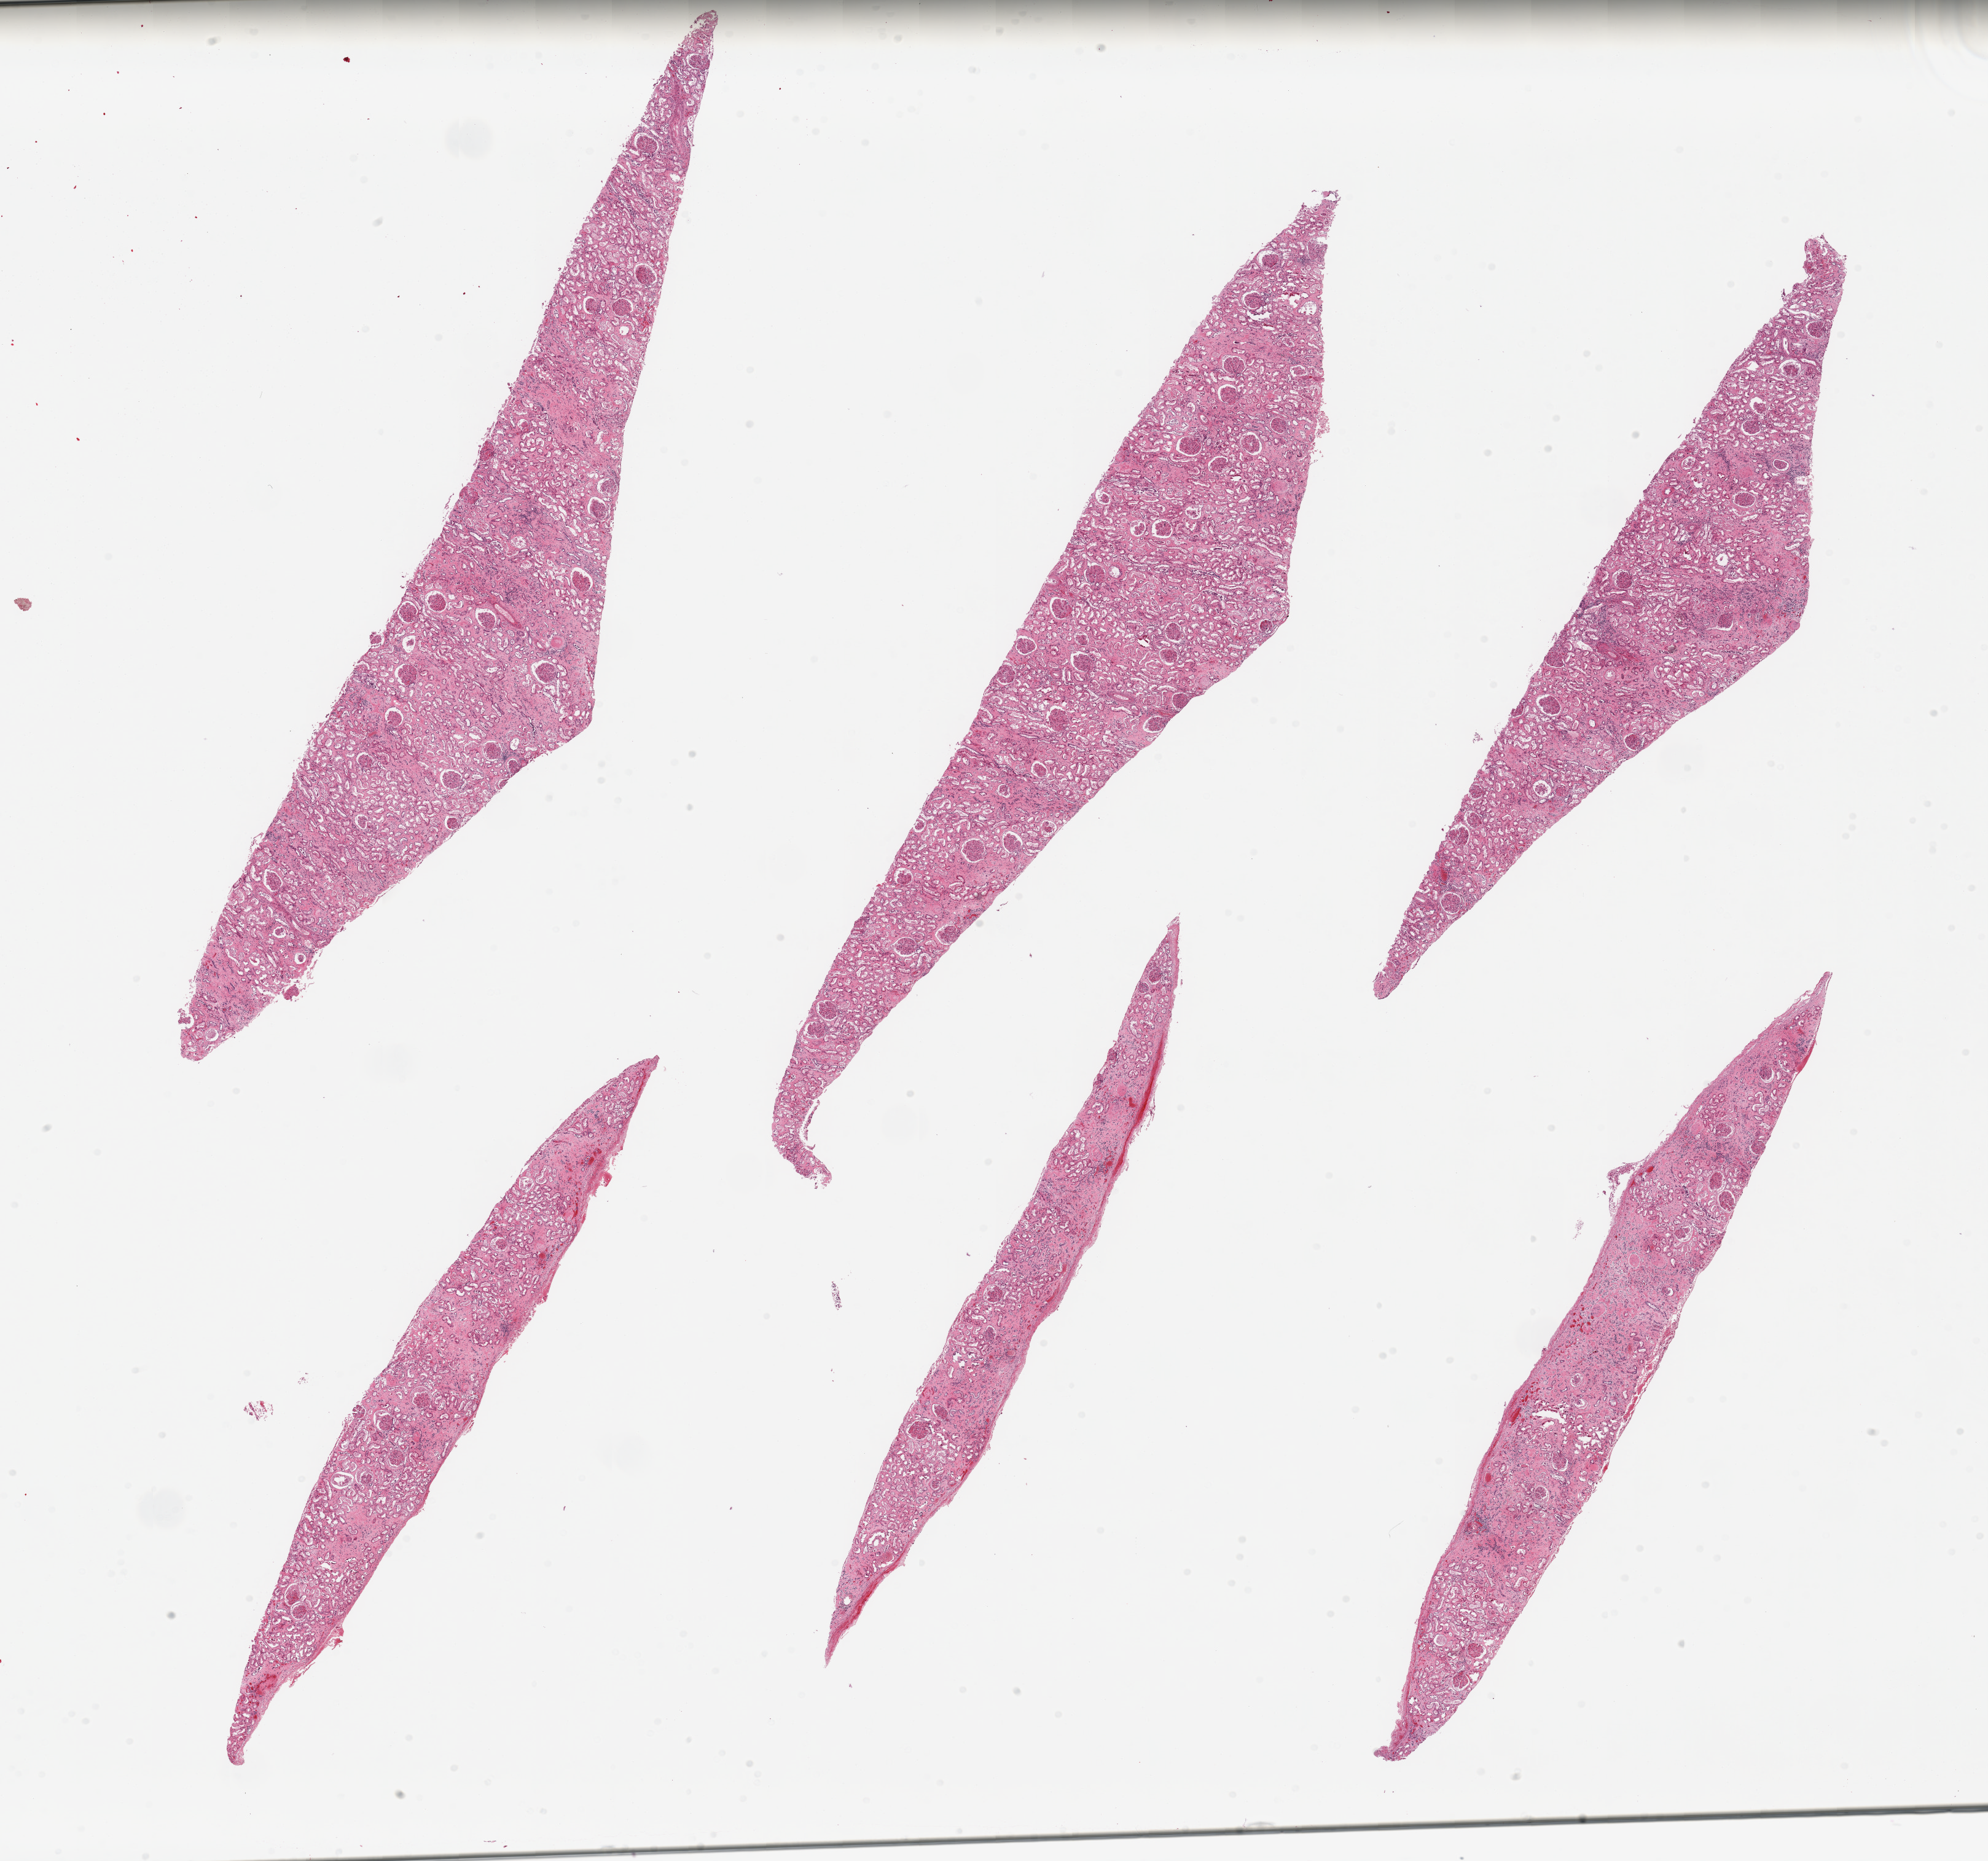
Digitized hematoxylin and eosin (H&E)-stained section, brightfield, low-resolution overview of the scanned area, about 25.6 x 24.0 mm (from a 20x scan). PAXgene-fixed paraffin-embedded (PFPE) section. Section of renal cortex (target tissue). Donor tissue sample. Male donor.
Review note (as recorded): 6 pieces; moderate interstitial fibrosis.